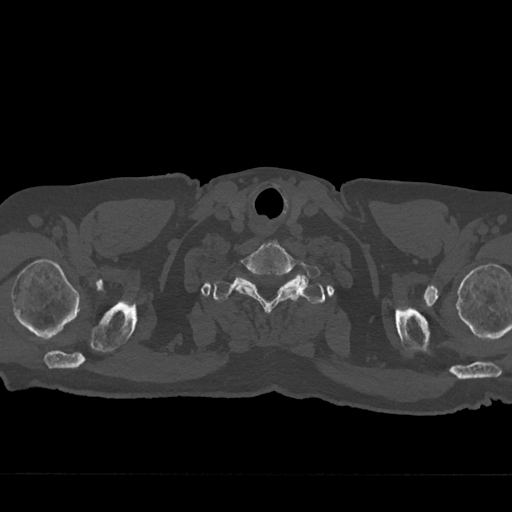
CT including the spine, one axial slice; slice 680 of 797 in the series (ordered by position); reconstruction kernel Br40s/3; bone window (W 1800 / L 400 HU); 0.5 mm slice thickness; 512 × 512 image matrix. Male patient, age 75 years. Case-level facts recorded for this patient, not image findings: primary cancer: renal; vertebrae with lytic lesions (as recorded): T4.
Structures marked on this image (semi-automatic segmentation, software-assisted and operator-edited):
- T1 vertebra: bounding box (x1, y1, x2, y2) in pixels: (213, 277, 323, 303)